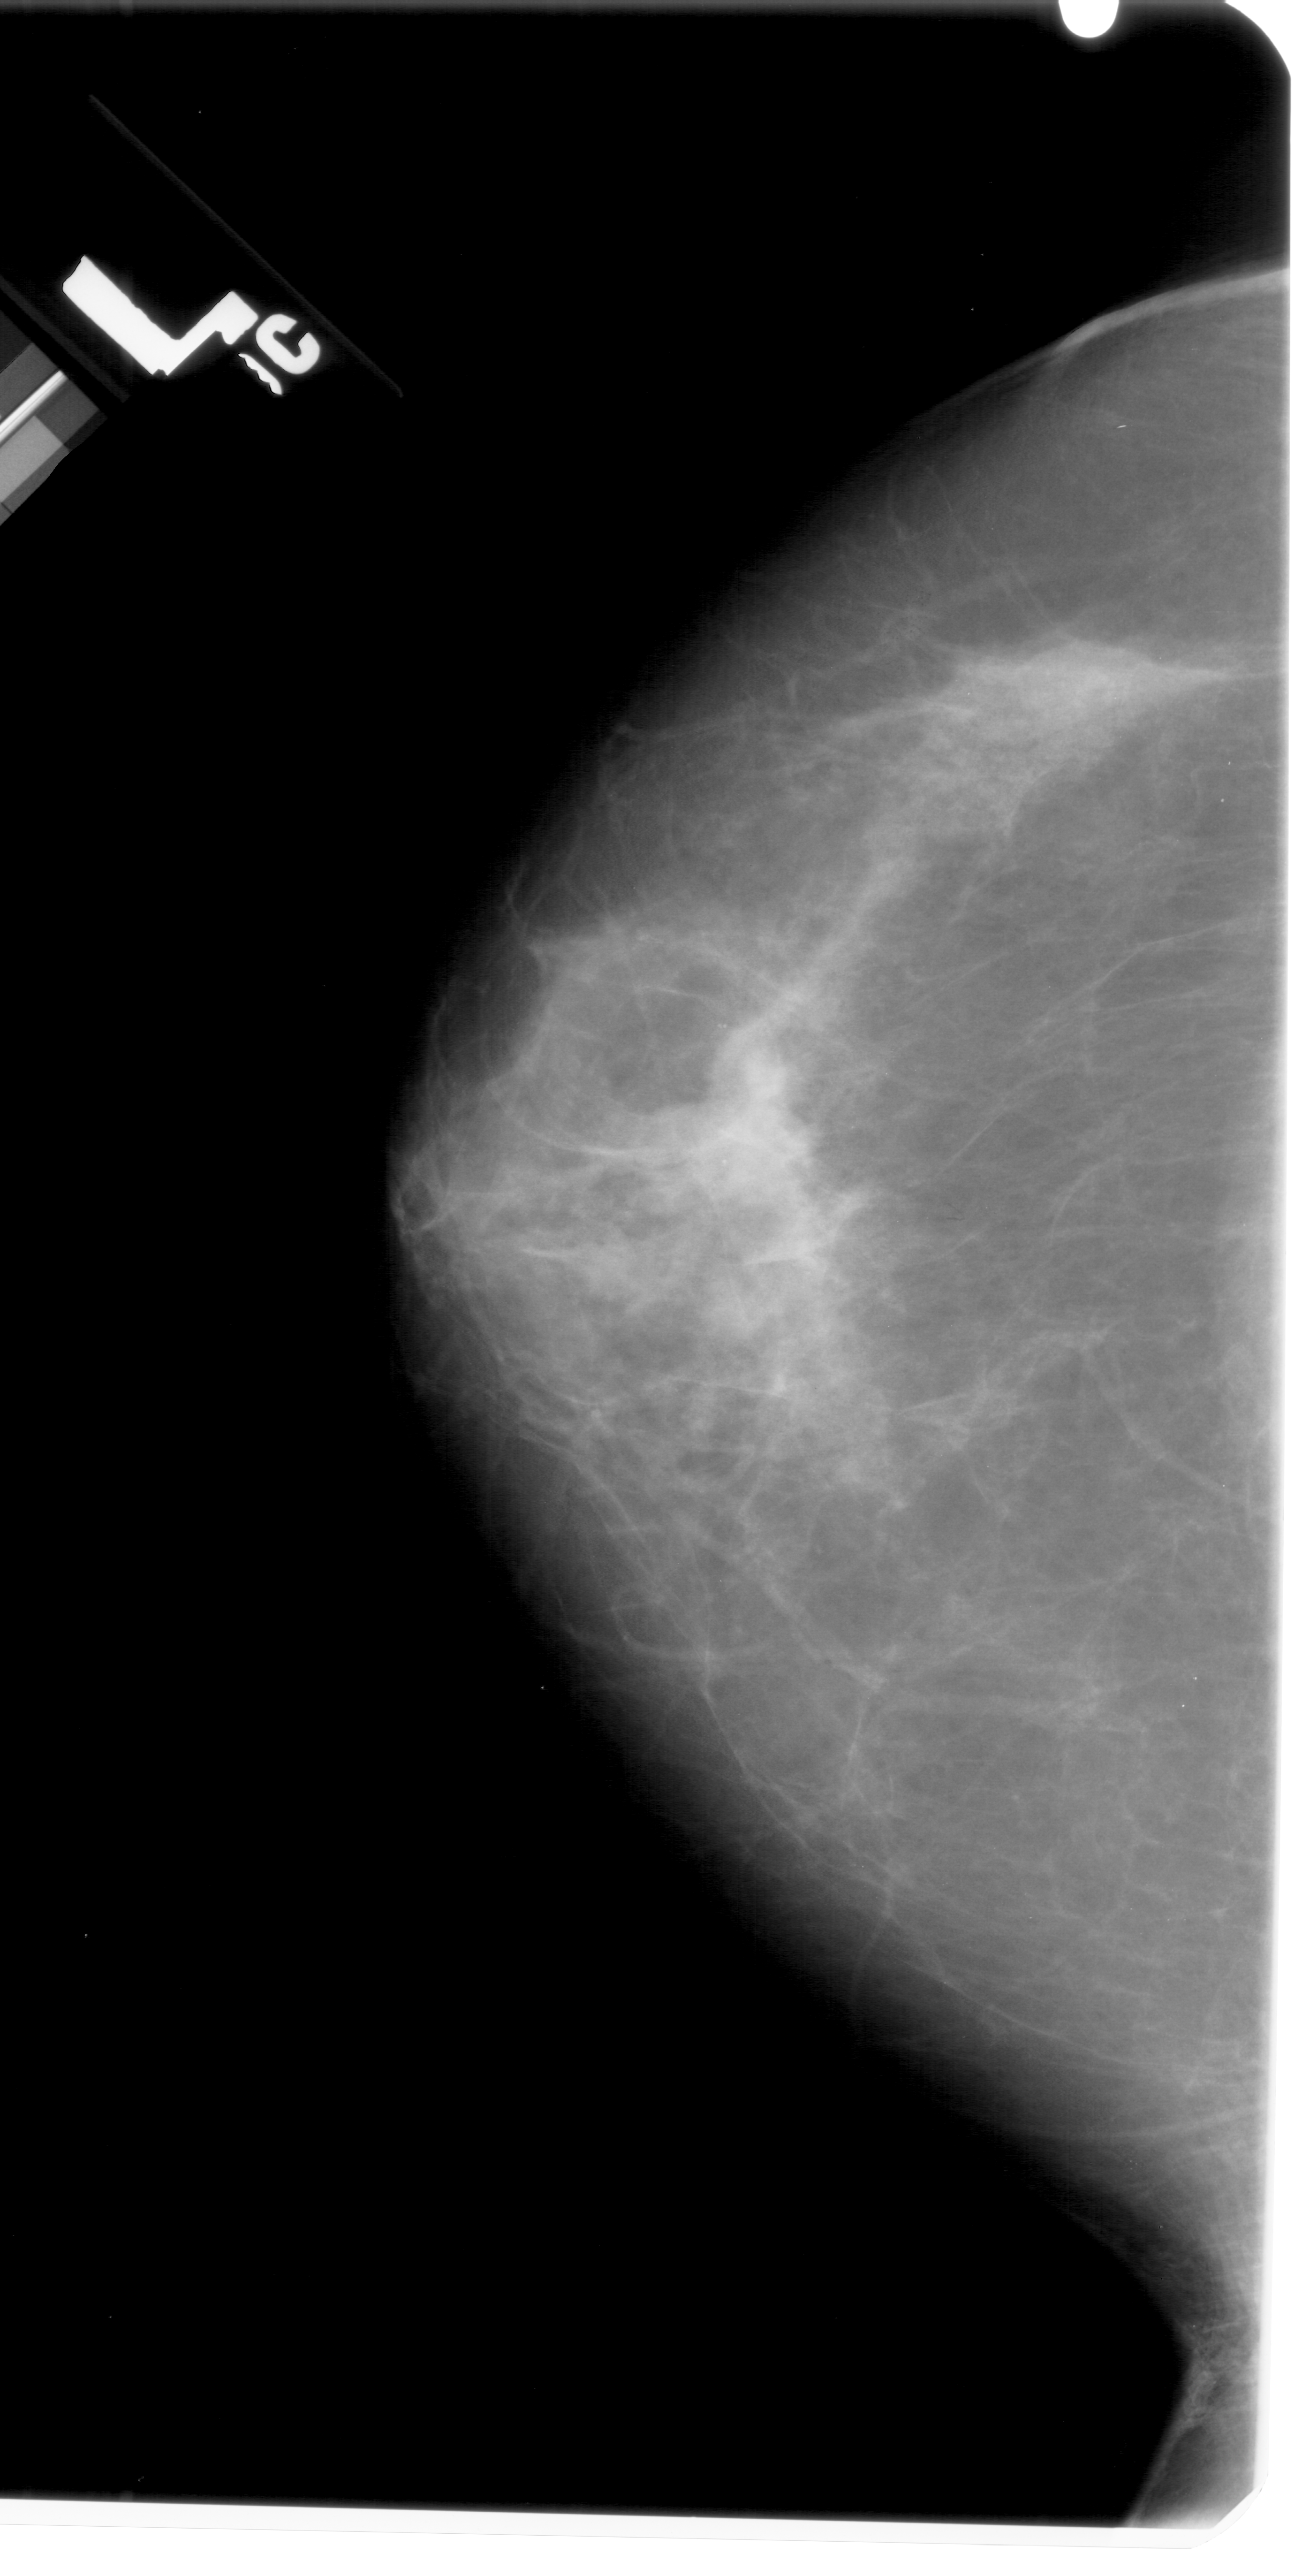
Digitized screen-film mammogram, left breast, craniocaudal (CC) view.
Abnormality record for this image: mass, shape irregular, margins ill defined; BI-RADS assessment category 4; pathology result (as recorded, not read from the image): malignant.